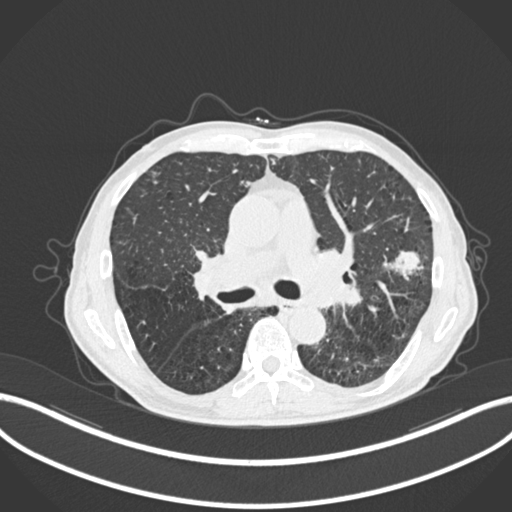
Chest CT, one axial slice. Position 148 of 287 along the scan axis. 120 kVp. Lung window (W 1500 / L -600 HU). 1 mm slice thickness. 512 × 512 image matrix, field of view 400 × 400 mm. Patient: male, 74 years. Case-level facts recorded for this patient, not image findings: clinical TNM (as recorded): T2a N1 M0.
Structures marked on this image (rectangle marked by the reading radiologist):
- lung tumour (recorded histology: adenocarcinoma): bounding box [x1, y1, x2, y2] px = [380, 246, 423, 280]